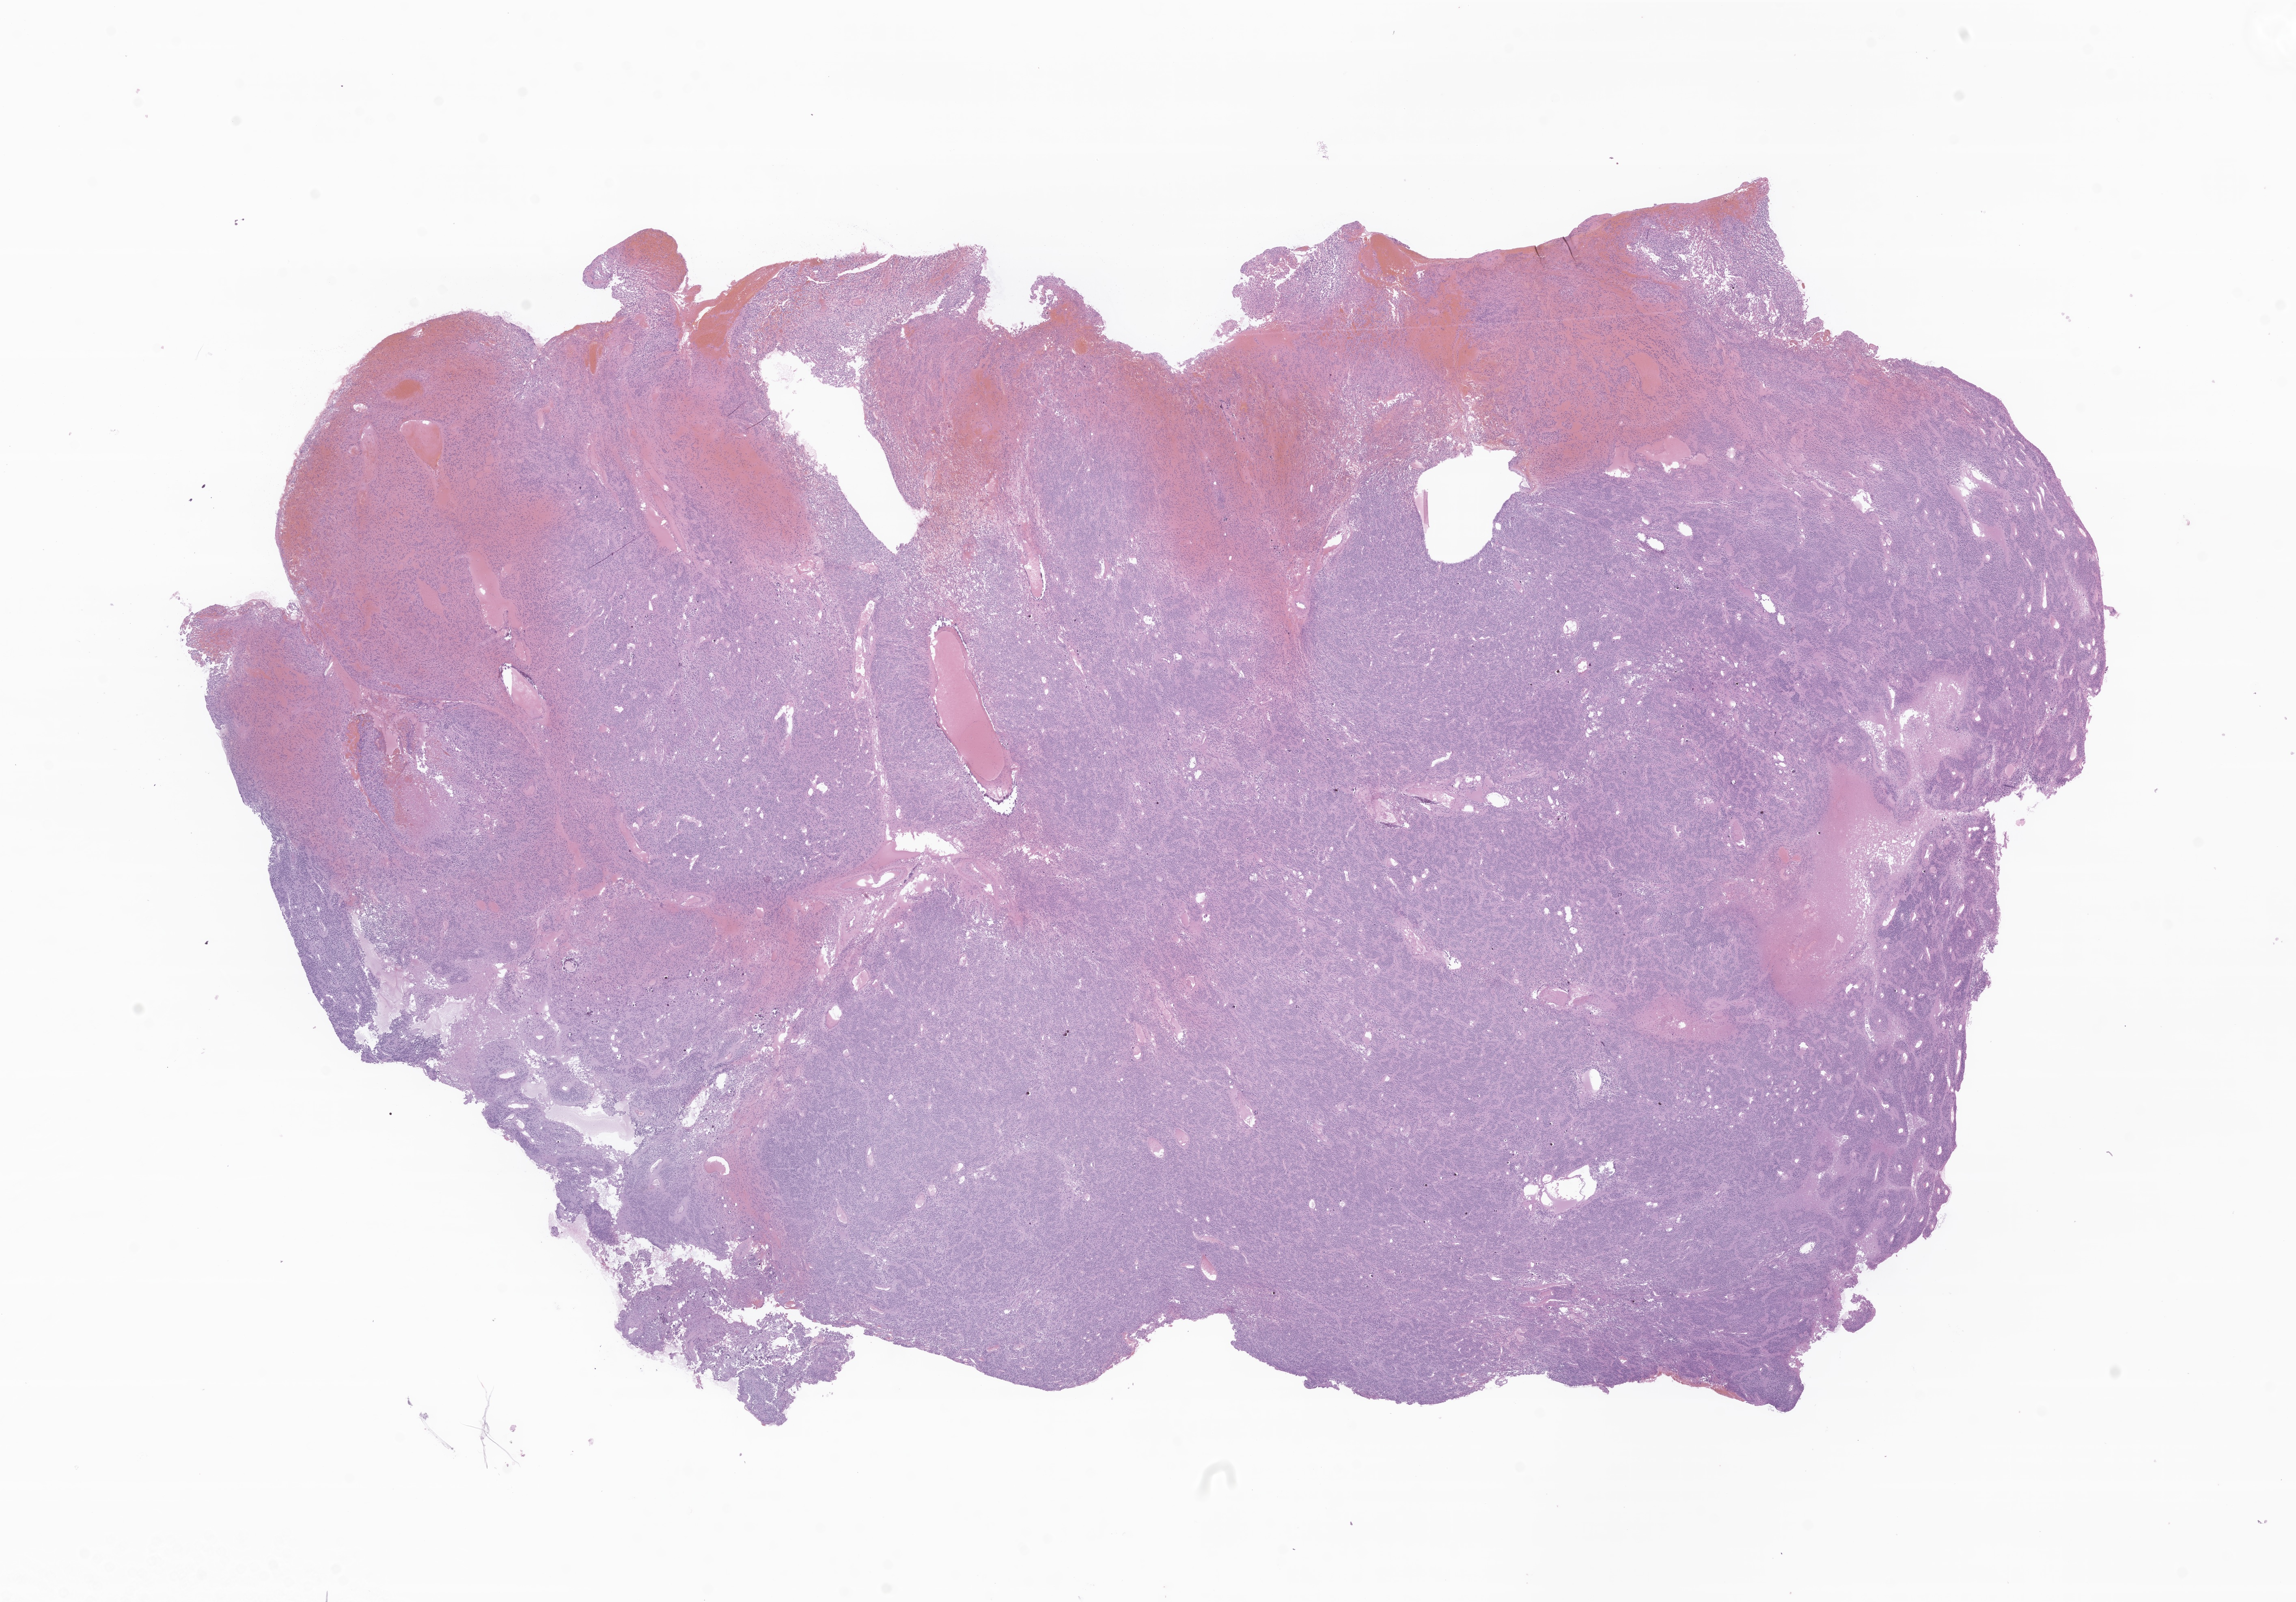
Haematoxylin and eosin whole-slide image of tumor tissue from the brain, a low-resolution overview of the entire scanned area, about 23.8 x 16.6 mm; formalin-fixed, paraffin-embedded (FFPE) tissue. Female patient, age 237 months (19 years 9 months).
Diagnosis: Glioma, malignant.